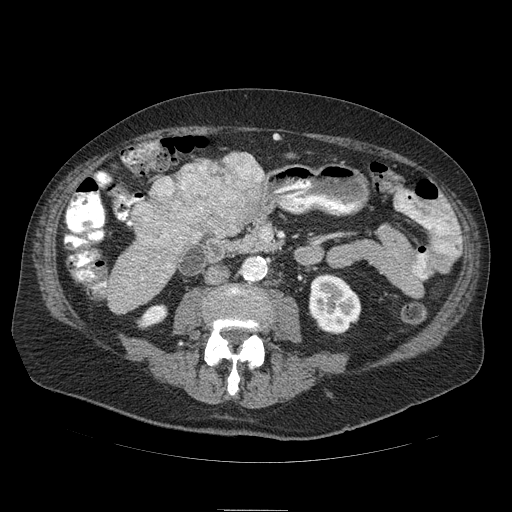
Contrast-enhanced abdominal CT (liver protocol), one axial slice; slice 18 of 103 in the series (ordered by position); 120 kVp; soft-tissue window (W 400 / L 40 HU); 2.5 mm slice thickness; 512 × 512 image matrix. Case-level facts recorded for this patient, not image findings: diagnosis: hepatocellular carcinoma (patient treated with transarterial chemoembolisation; whether this scan precedes or follows treatment is not stated here); TNM stage (as recorded): Stage-IIIA; Child-Pugh class: B; tumour nodularity: multinodular; tumour size: 13 cm.
Outlined on this slice (semi-automatic segmentation, software-assisted and operator-edited):
- liver parenchyma outside the tumour (the mass and vessels are separate outlines, so this box may not span the whole liver): bounding box <217,153,264,178> (left, top, right, bottom; pixels)
- mass: <132,154,266,263>